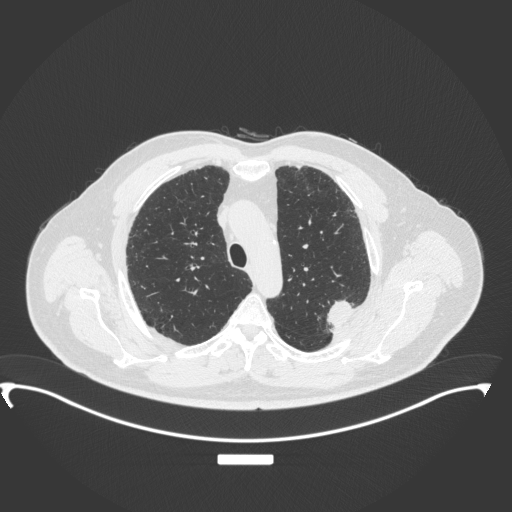
Chest CT, one axial slice; position 271 of 350 along the scan axis; reconstruction kernel B31f; 120 kVp; lung window (W 1500 / L -600 HU); 1 mm slice thickness; 512 × 512 image matrix. Patient: male, 64 years. From the clinical record (not read from this slice): clinical TNM (as recorded): T1c N1 M1.
Structures marked on this image (rectangle marked by the reading radiologist):
- lung tumour (recorded histology: adenocarcinoma): bounding box (x1, y1, x2, y2) in pixels: (319, 295, 363, 338)